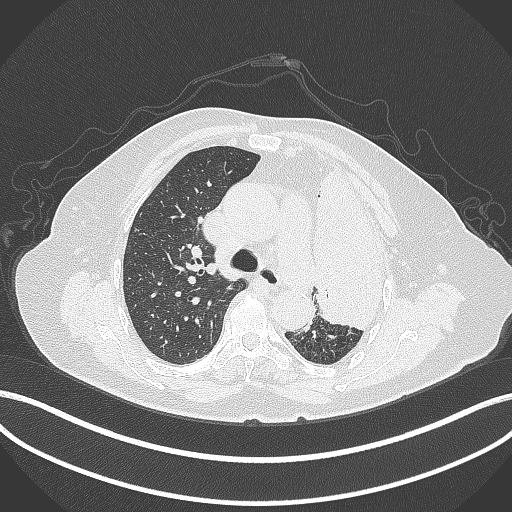
Chest CT, one axial slice. Position 266 of 399 along the scan axis. Reconstruction kernel B70f. 120 kVp. Lung window (W 1500 / L -600 HU). 1 mm slice thickness. 512 × 512 image matrix, field of view 400 × 400 mm. Female patient, age 75 years. From the clinical record (not read from this slice): clinical TNM (as recorded): T3 N3 M1.
Structures marked on this image (rectangle marked by the reading radiologist):
- lung tumour (recorded histology: adenocarcinoma): bounding box [x1, y1, x2, y2] px = [304, 161, 400, 333]